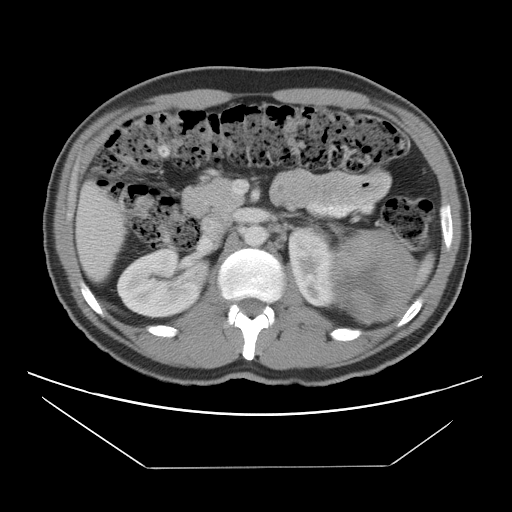
Contrast-enhanced abdominal CT, one axial slice; slice 65 of 131 in the series (ordered by position); reconstruction kernel STANDARD; 120 kVp; intravenous contrast given; soft-tissue window (W 400 / L 40 HU); 5 mm slice thickness; 512 × 512 image matrix, field of view 396 × 396 mm. Patient: male, 44 years. From the clinical record (not read from this slice): diagnosis: adrenocortical carcinoma; tumour side: left adrenal; tumour size at pathology: 15.5 cm; Ki-67 index: 6 %; stage (as recorded): 2.
Annotated regions visible in this slice (semi-automatic segmentation, software-assisted and operator-edited):
- mass: bounding box <334,230,412,322> (left, top, right, bottom; pixels)